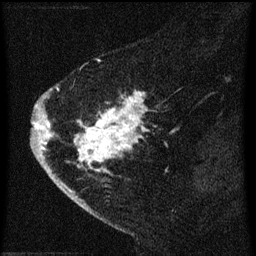
Breast MRI (dynamic contrast-enhanced), one sagittal slice; slice 18 of 60 in the series (ordered by position); dynamic contrast-enhanced series, image 2 of 3 at this slice position (ordered by acquisition); 1.5 T; TE 4.2 ms, TR 8 ms; 2 mm slice thickness; 256 × 256 image matrix. Patient: female, 47 years.
Structures marked on this image (semi-automatic segmentation, software-assisted and operator-edited):
- analysis volume of interest (the breast-tissue region the enhancement analysis was run in; not a lesion): bounding box [x1, y1, x2, y2] px = [38, 78, 156, 193]
- tumour enhancement mask (voxels above the 70 % enhancement threshold inside the analysis volume of interest): [38, 92, 149, 193]